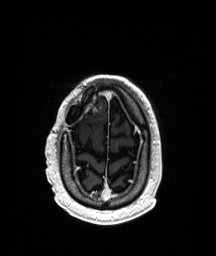
Brain MRI from a brain-tumour surgery series, one axial slice; position 36 of 192 along the scan axis; T1-weighted post-contrast; 1 mm slice thickness; 216 × 256 image matrix, field of view 211 × 250 mm. Case-level facts recorded for this patient, not image findings: histopathology: Astrocytoma; WHO grade: 3; IDH mutation: yes; tumour location: Right Frontal.
Annotated regions visible in this slice (expert manual segmentation):
- previous resection cavity: box from (x=87, y=110) to (x=94, y=116) px